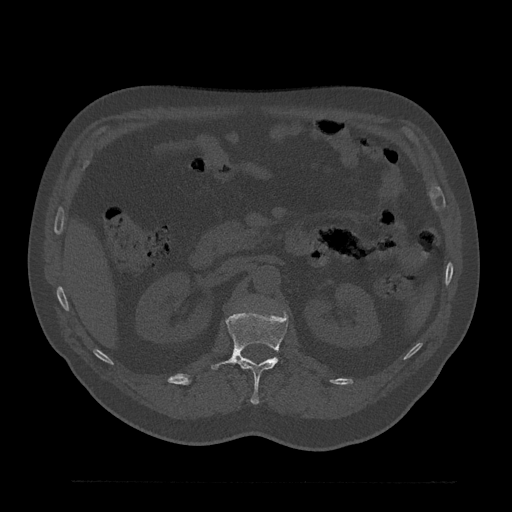
CT including the spine, one axial slice; position 158 of 797 along the scan axis; reconstruction kernel Br40s/3; bone window (W 1800 / L 400 HU); 0.5 mm slice thickness; 512 × 512 image matrix. Male patient, age 61 years. Case-level facts recorded for this patient, not image findings: primary cancer: prostate.
Structures marked on this image (semi-automatically segmented with operator editing):
- L1 vertebra: bounding box (x1, y1, x2, y2) in pixels: (210, 310, 288, 405)